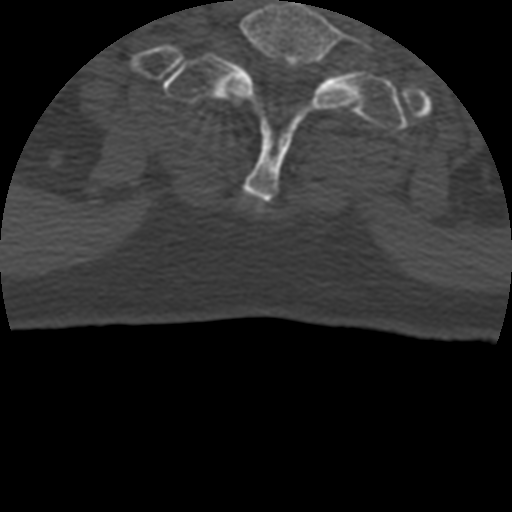
CT including the spine, one axial slice; reconstruction kernel STANDARD; 120 kVp; bone window (W 1800 / L 400 HU); 1.25 mm slice thickness; 512 × 512 image matrix, field of view 160 × 160 mm. Patient age 69 years. Case-level facts recorded for this patient, not image findings: primary cancer: prostate.
Annotated regions visible in this slice (semi-automatic segmentation, software-assisted and operator-edited):
- T1 vertebra: bounding box (x1, y1, x2, y2) in pixels: (161, 54, 408, 129)